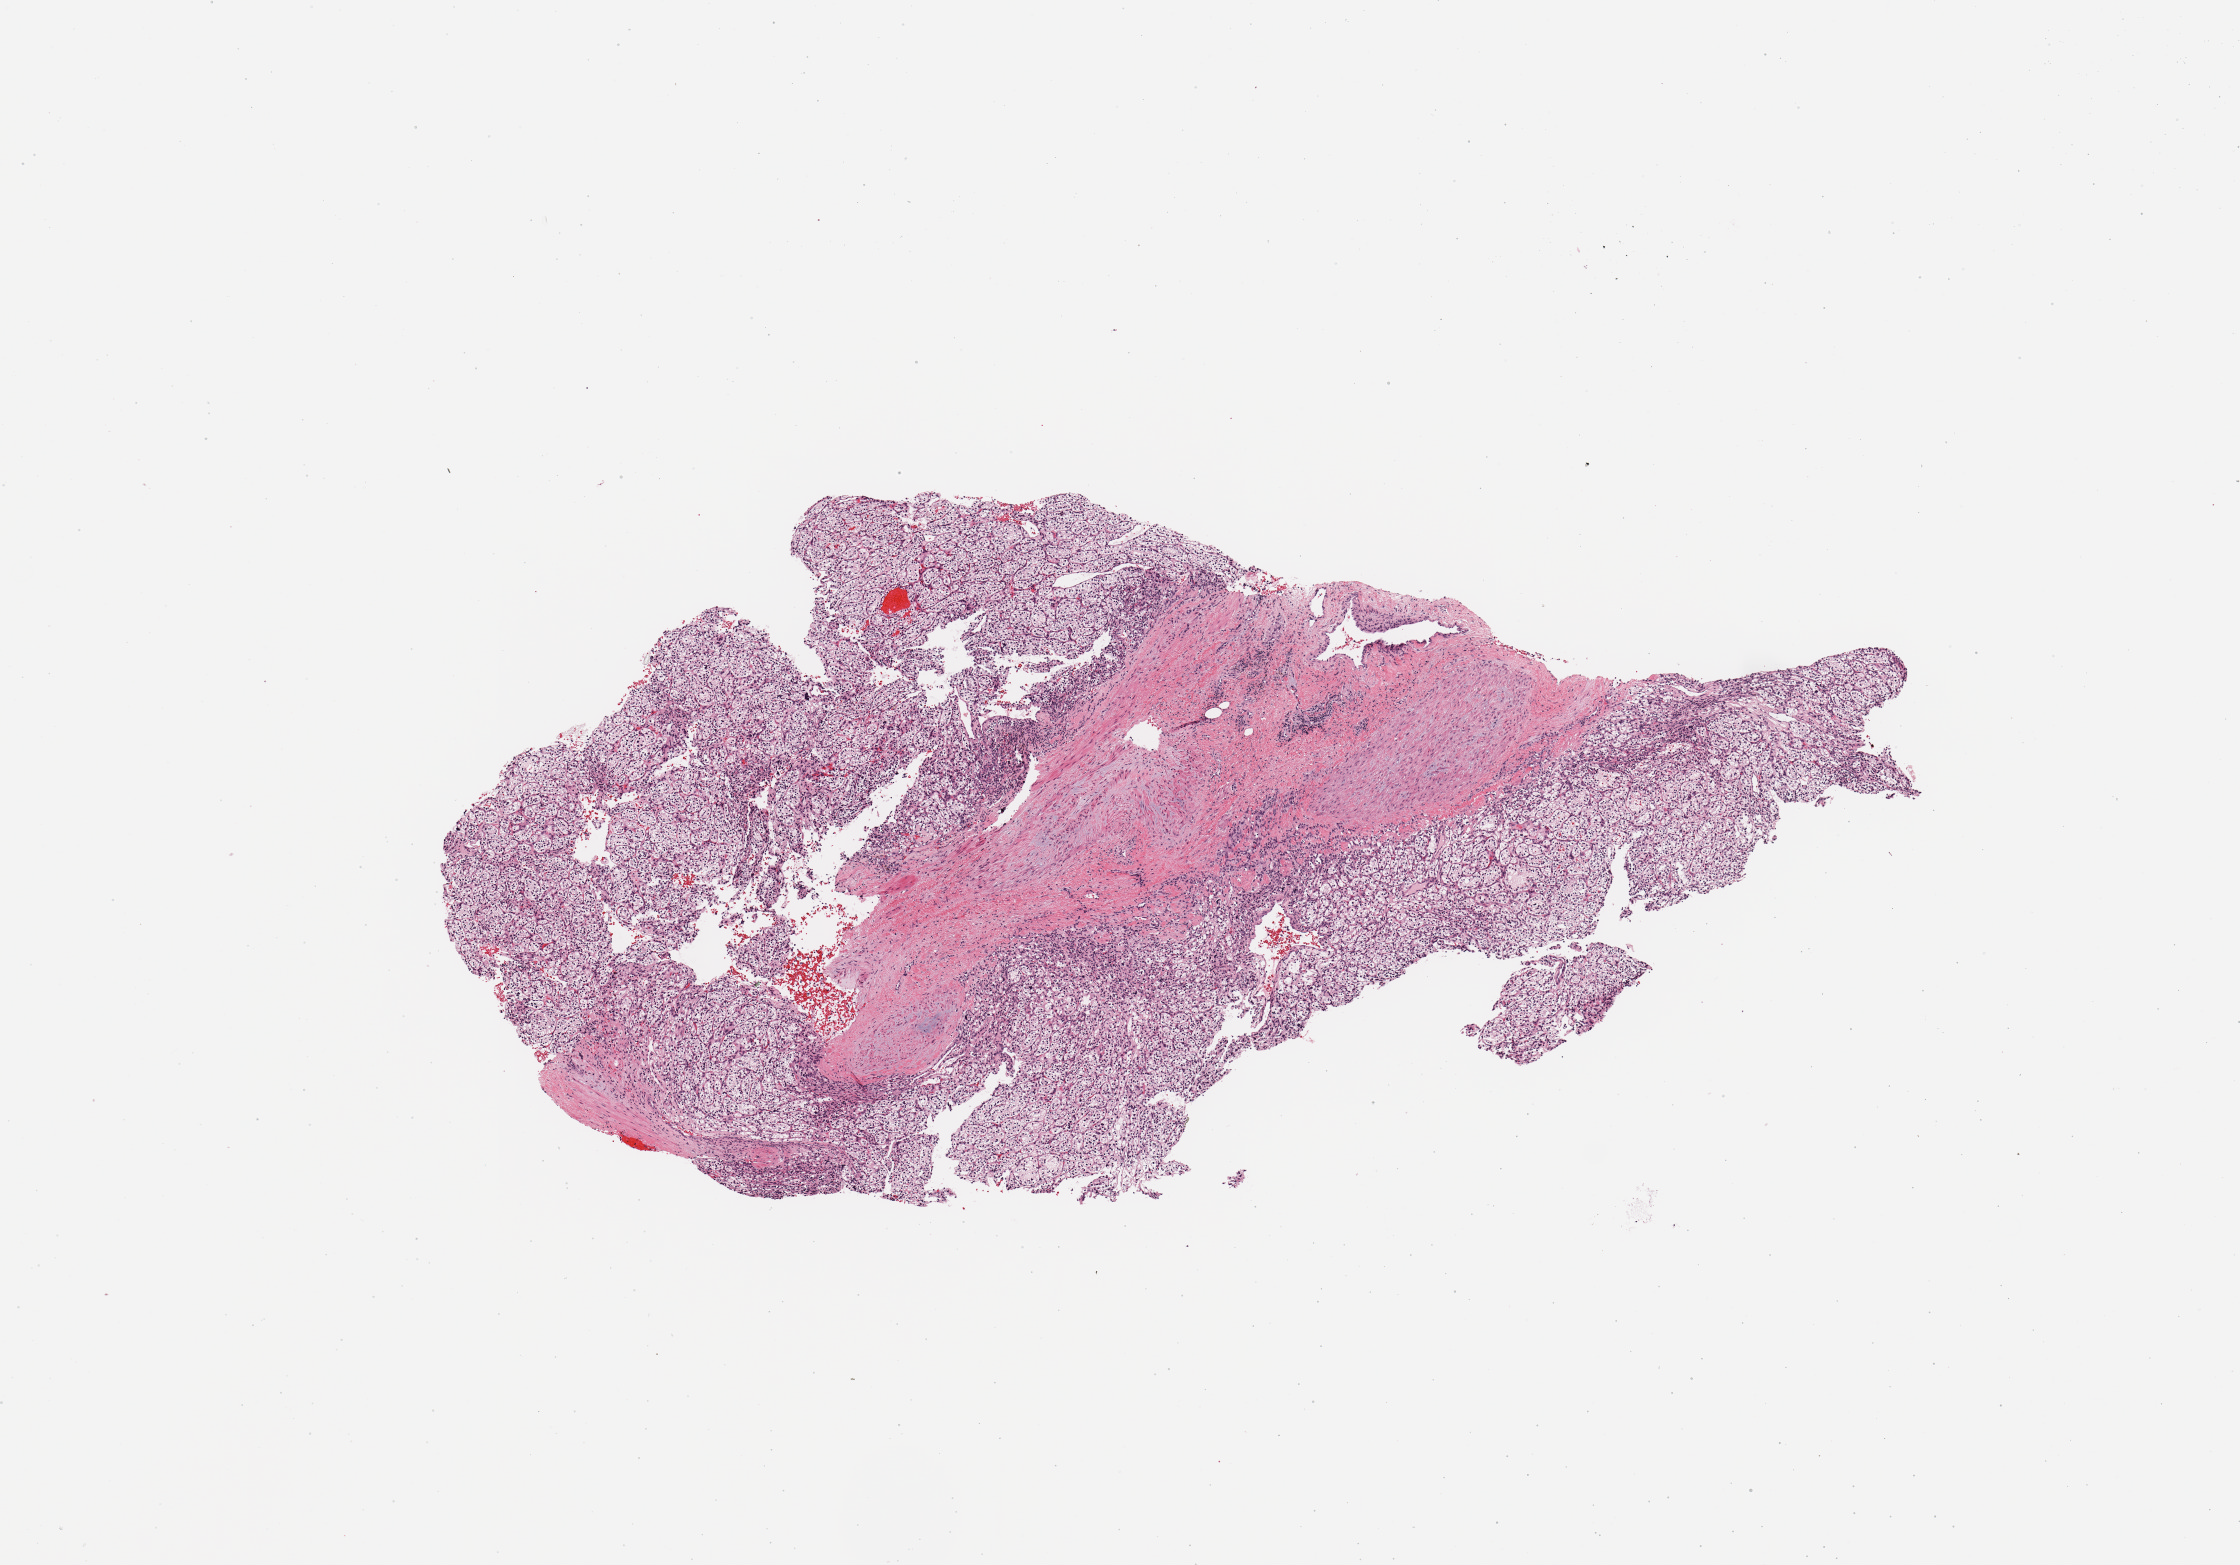
Digitized Hematoxylin and eosin (H&E) stained tissue section (whole slide) — whole scanned area (about 8.9 x 6.2 mm, acquisition: 20x scan) shown as a low-resolution overview; tumour tissue sample, sampled site: kidney. Patient: female, age 54 years. Slide review estimates, as recorded: tumour nuclei 80%, necrosis 5%.
Diagnosis: Renal cell carcinoma, NOS.